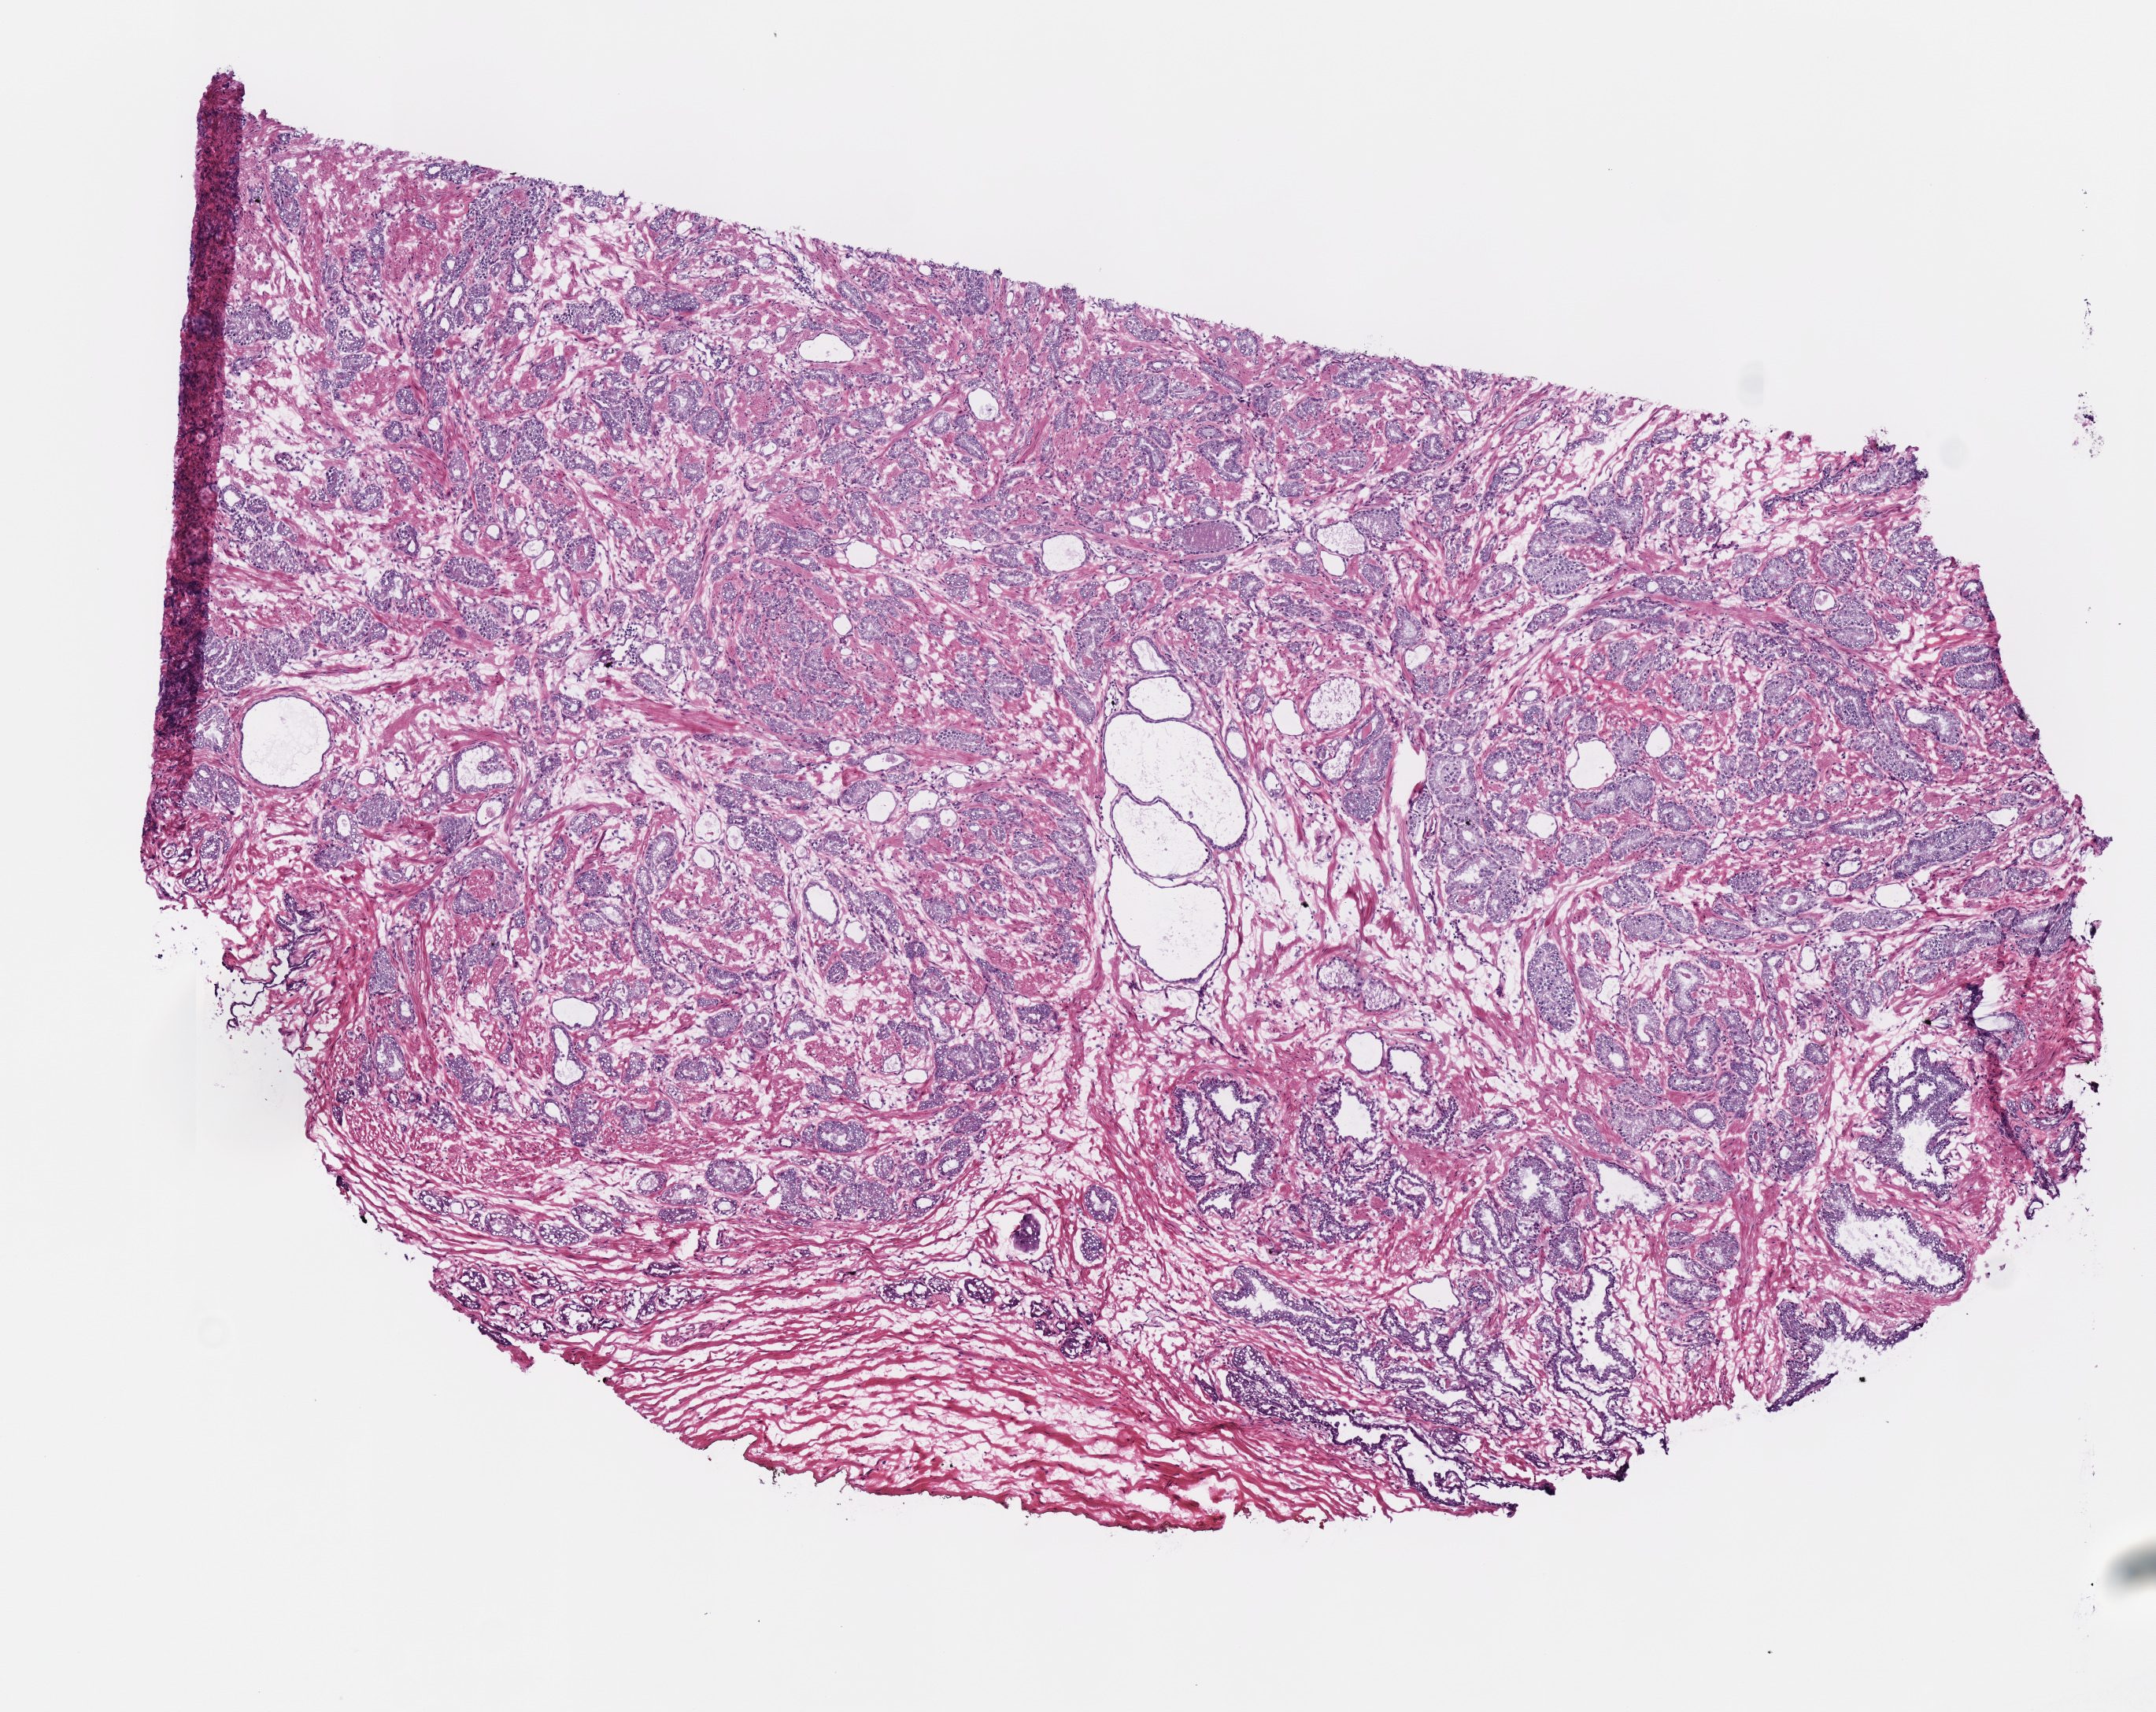
Whole-slide histology image, Hematoxylin and eosin (H&E) stained, low-resolution overview of the scanned area, about 5.4 x 4.3 mm (from a 40x scan). Frozen section from the bottom of the tissue portion. Primary tumour sample from the prostate. Male, age 59 years at initial diagnosis. Gleason score: 7 (3+4).
* lymph nodes positive (case pathology): 0 of 4 examined
* pathologic diagnosis: Acinar cell carcinoma (prostate gland)
* laterality: bilateral